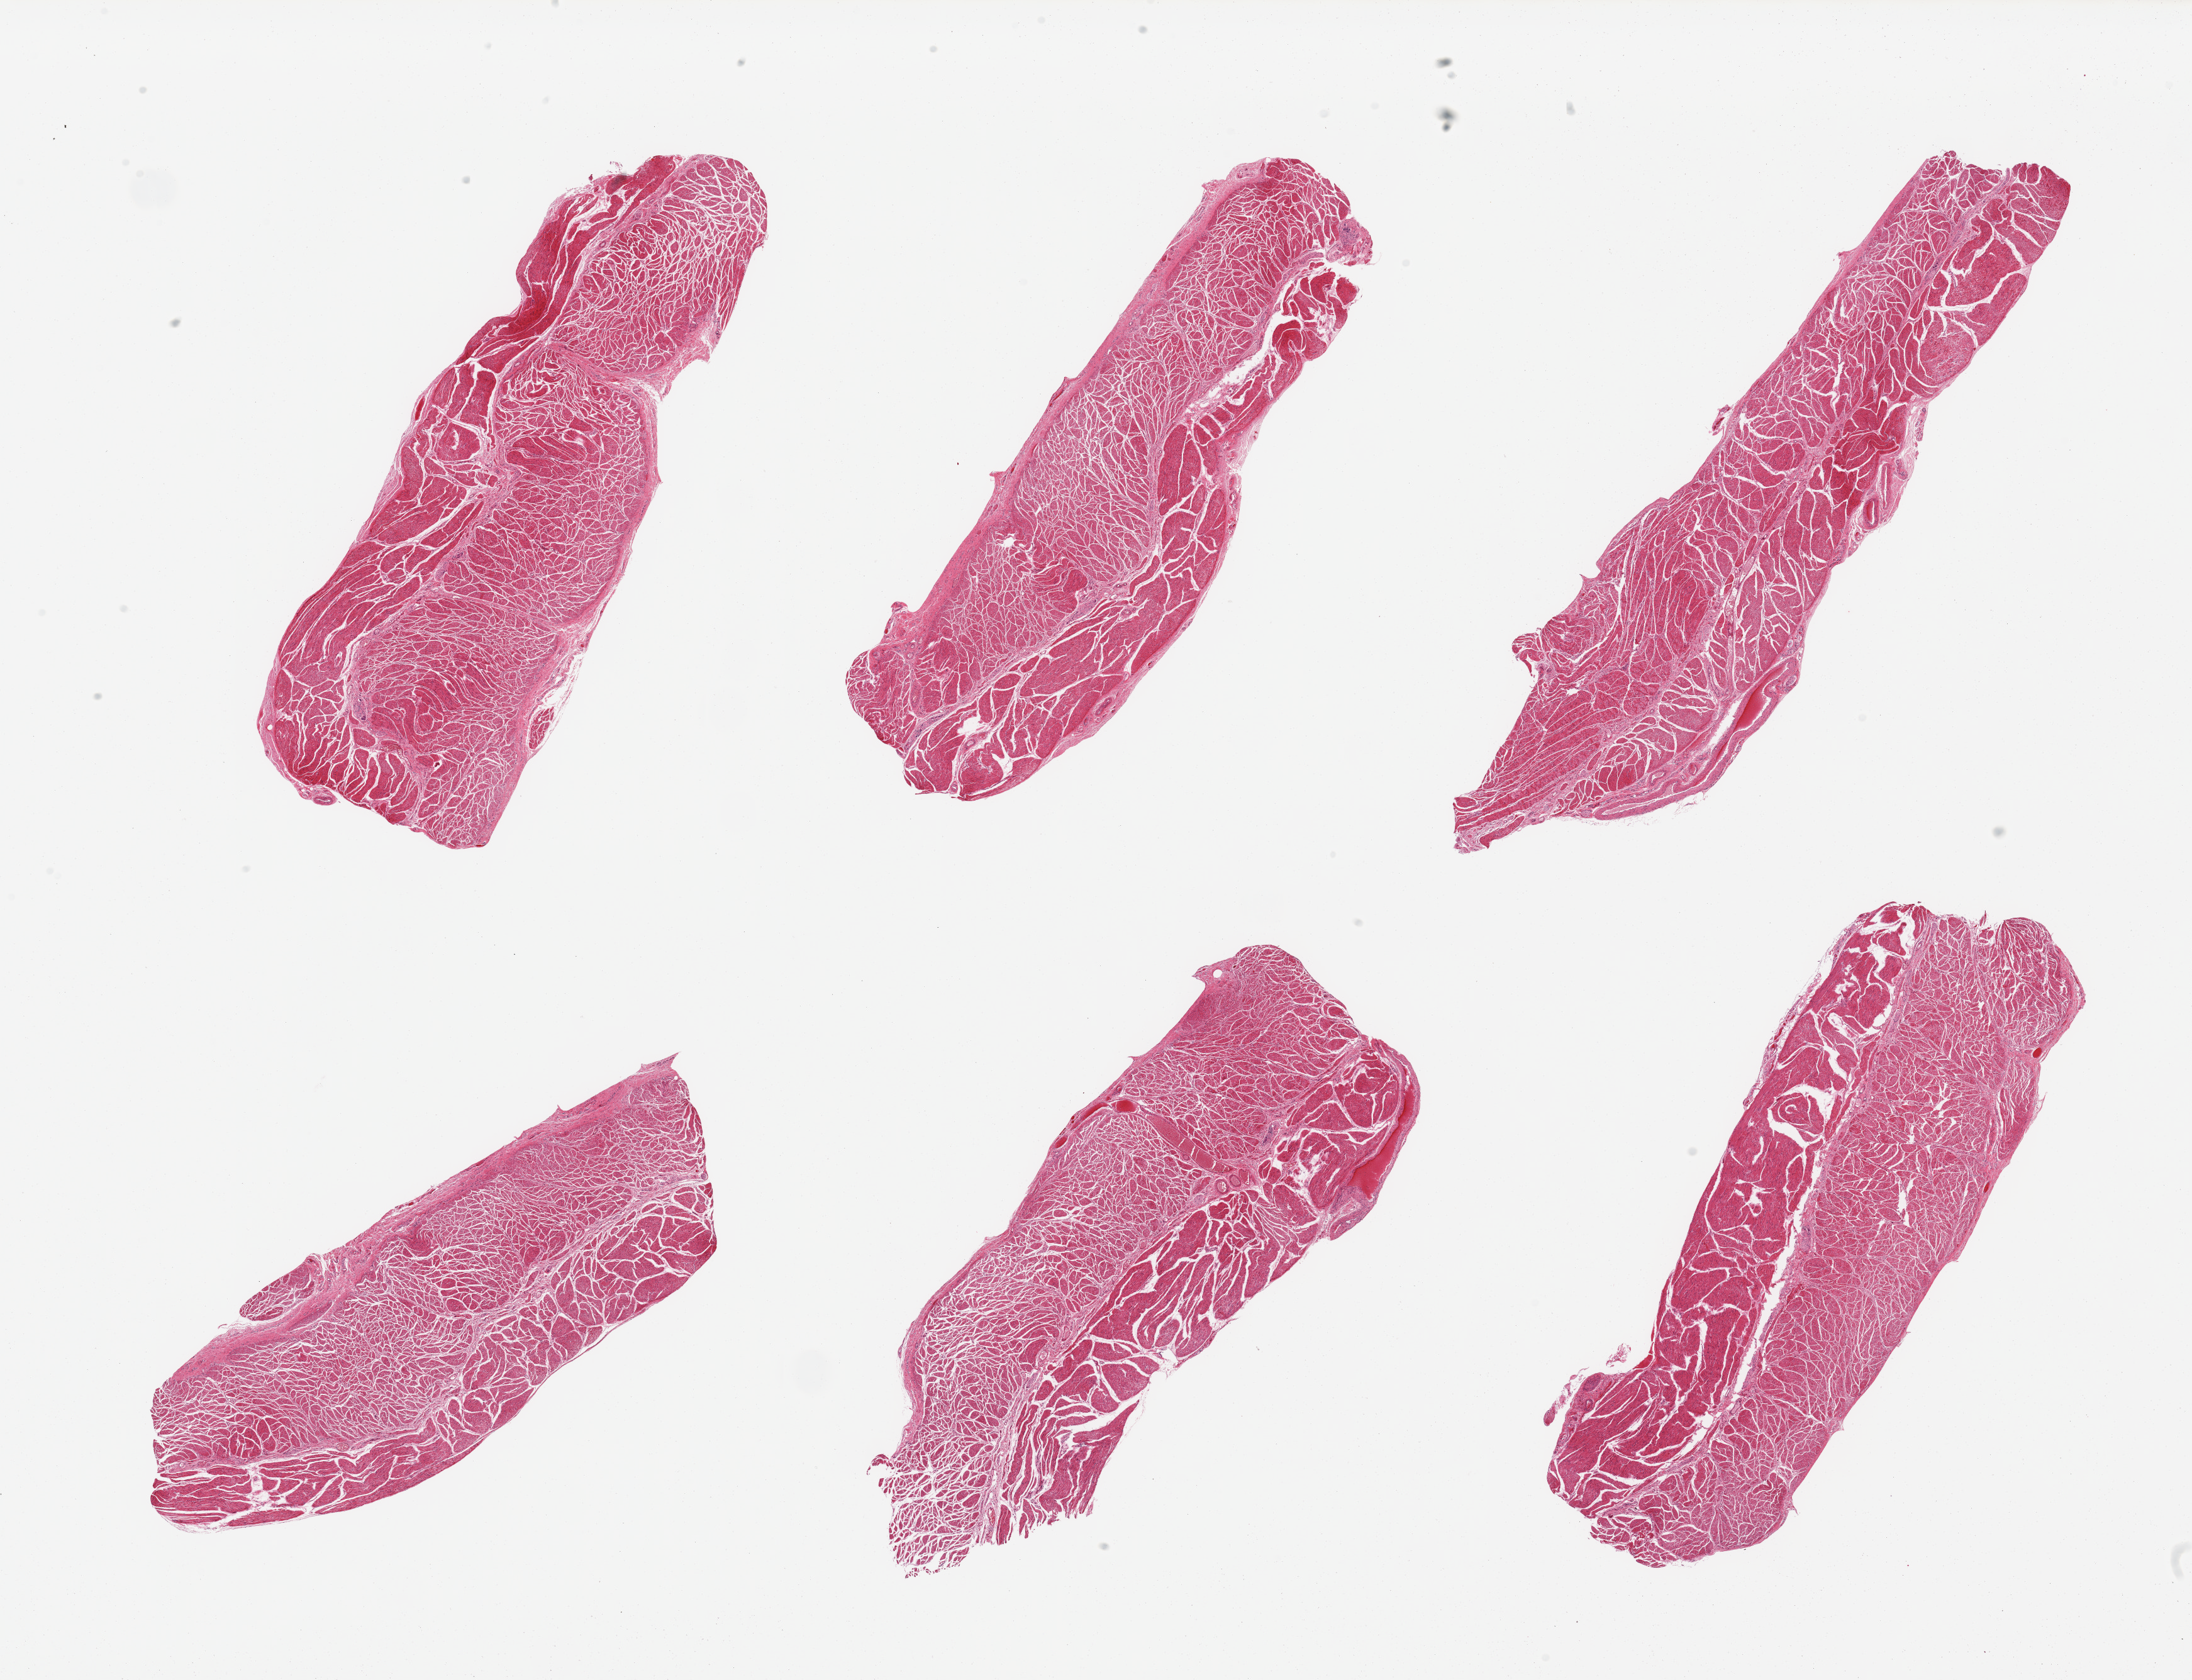
Hematoxylin and eosin (H&E) whole-slide image — shown as a low-resolution overview of the whole scanned area (about 27.6 x 21.1 mm). PAXgene-fixed, paraffin-embedded tissue. Sampled site (target tissue): gastroesophageal junction. Tissue donor sample. Donor: male.
• reviewer comment on this tissue sample: 6 pieces; well dissected